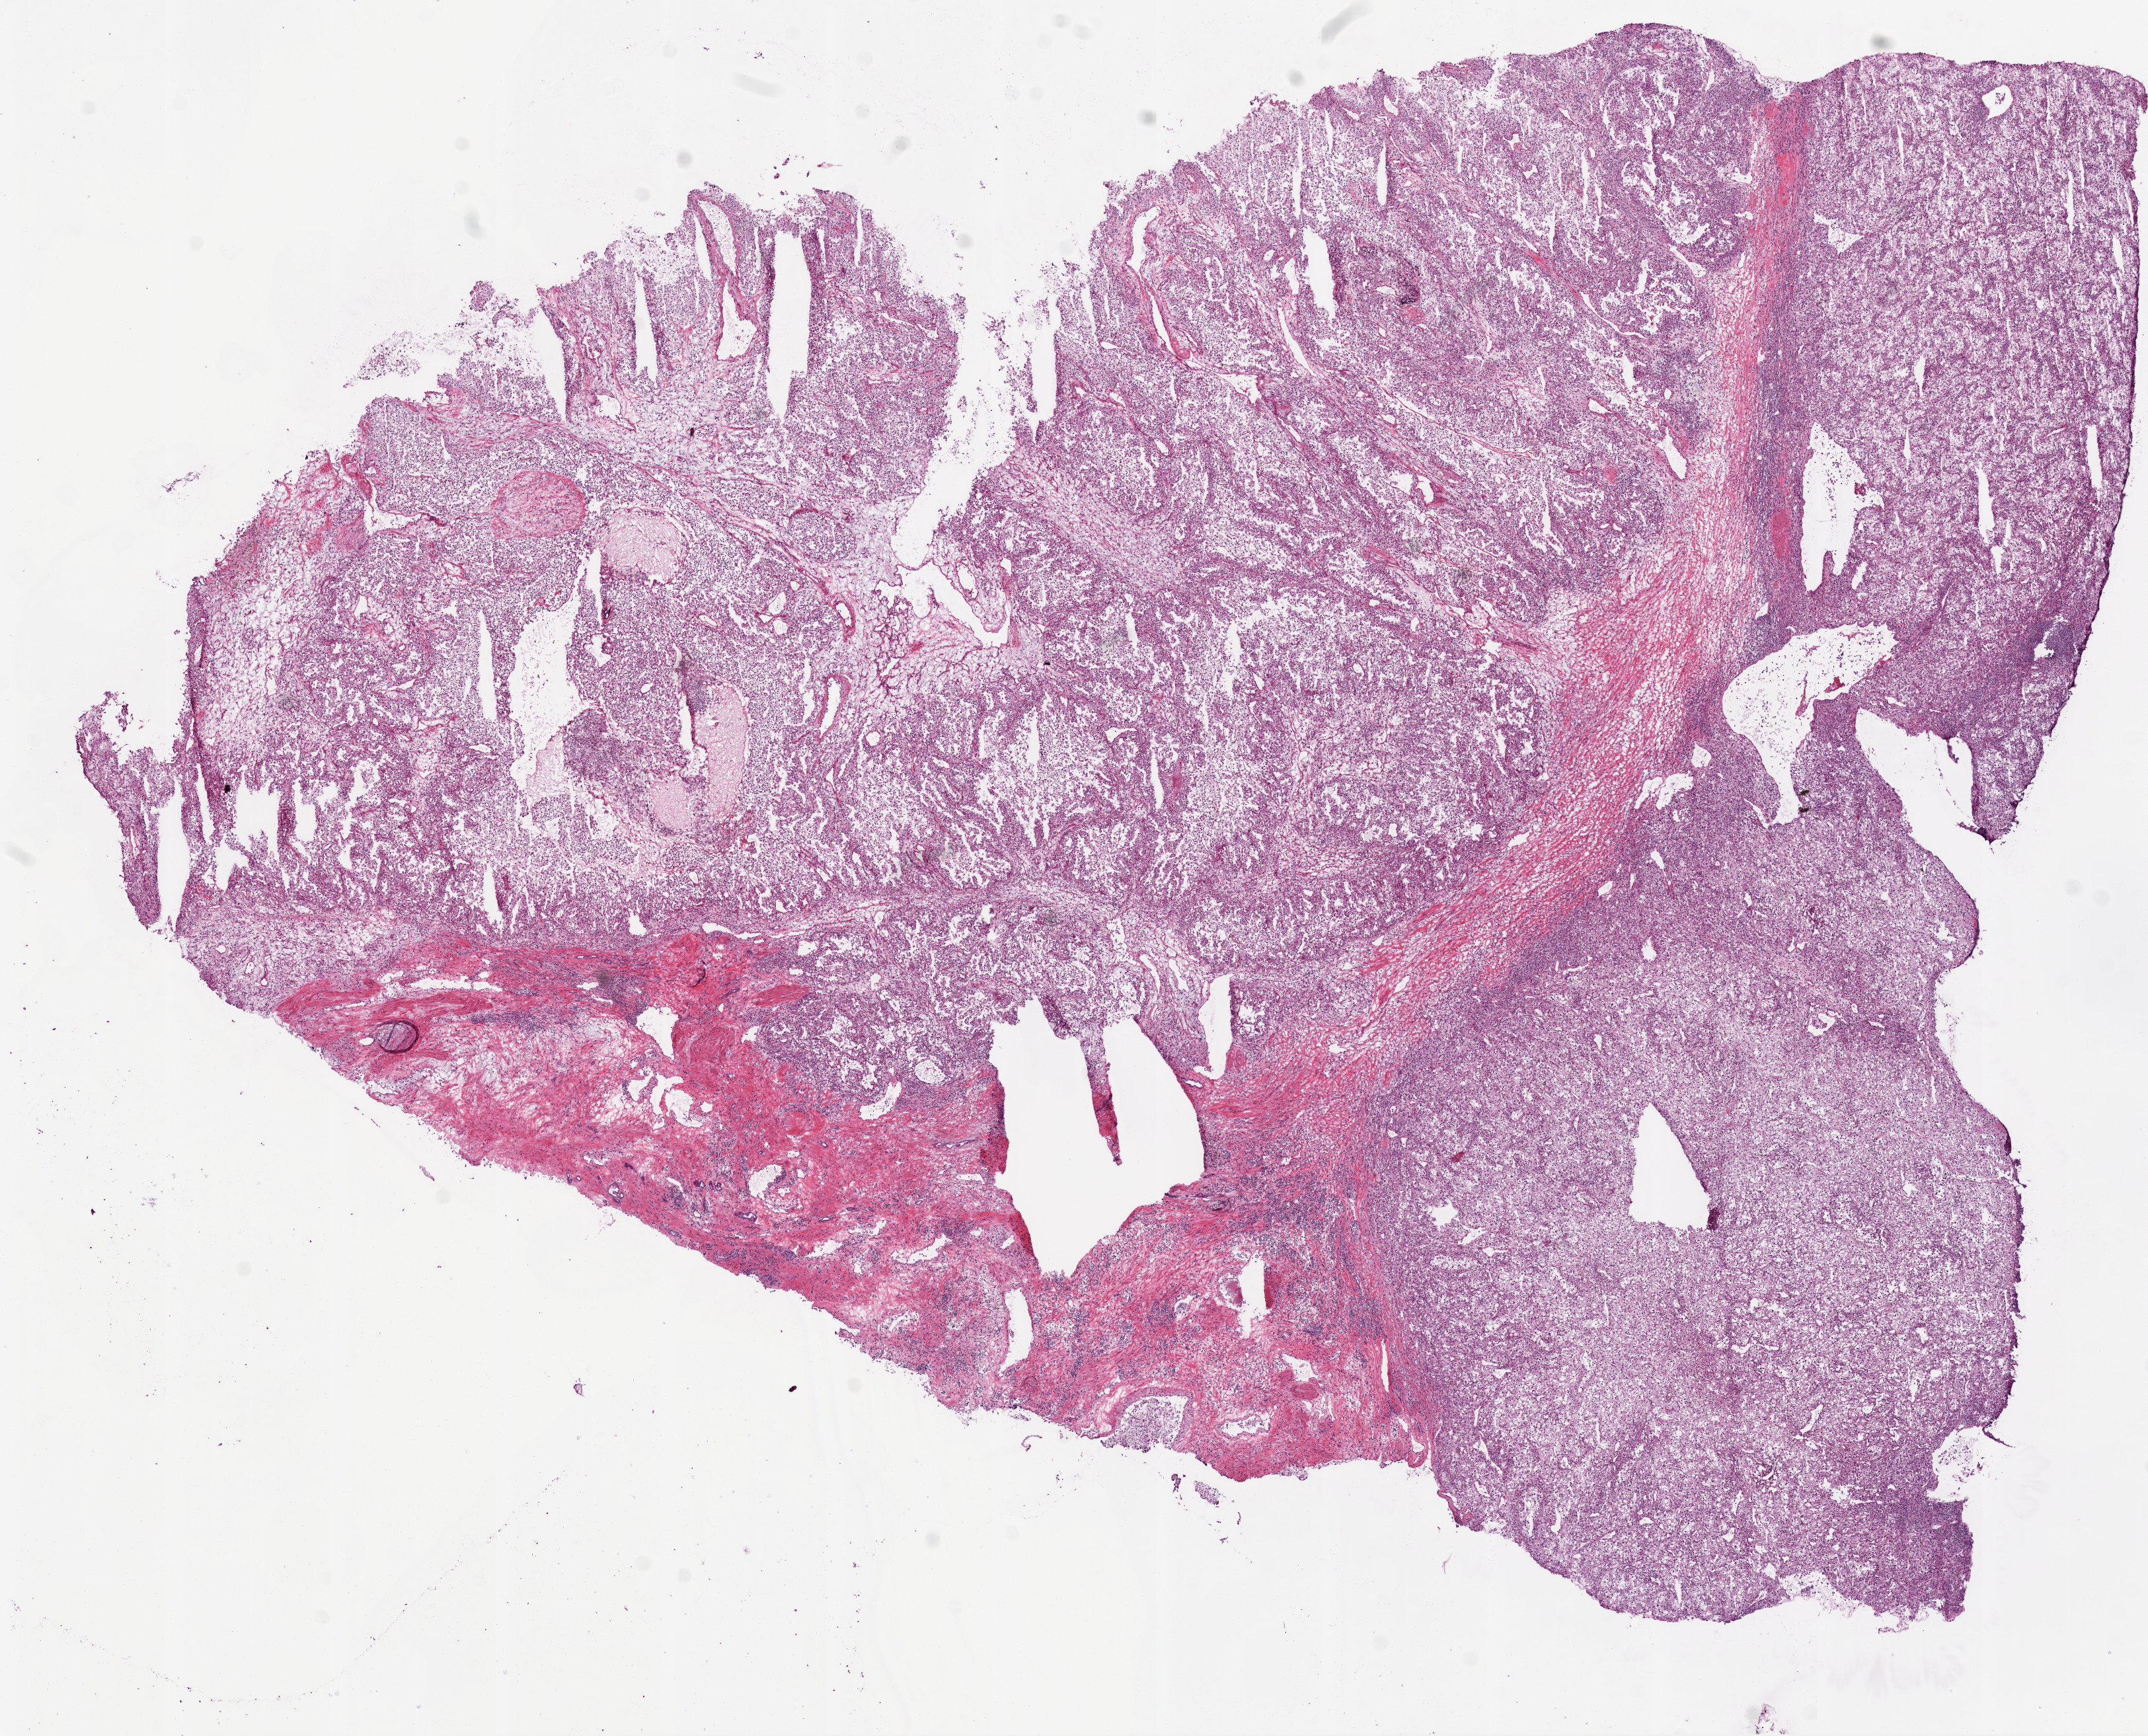
Whole-slide histology image, H&E-stained — whole scanned area (about 13.0 x 10.5 mm, from a 20x scan) shown as a low-resolution overview, frozen section, sample: primary tumour, kidney. Male, age 47 years at initial diagnosis. Histologic grade: G3 (poorly differentiated). Slide review estimates, as recorded: tumour cells 85%, tumour nuclei 75%, normal cells 0%, stromal cells 15%, necrosis 0%.
- AJCC pathologic stage: II
- diagnosis: Clear cell adenocarcinoma, NOS